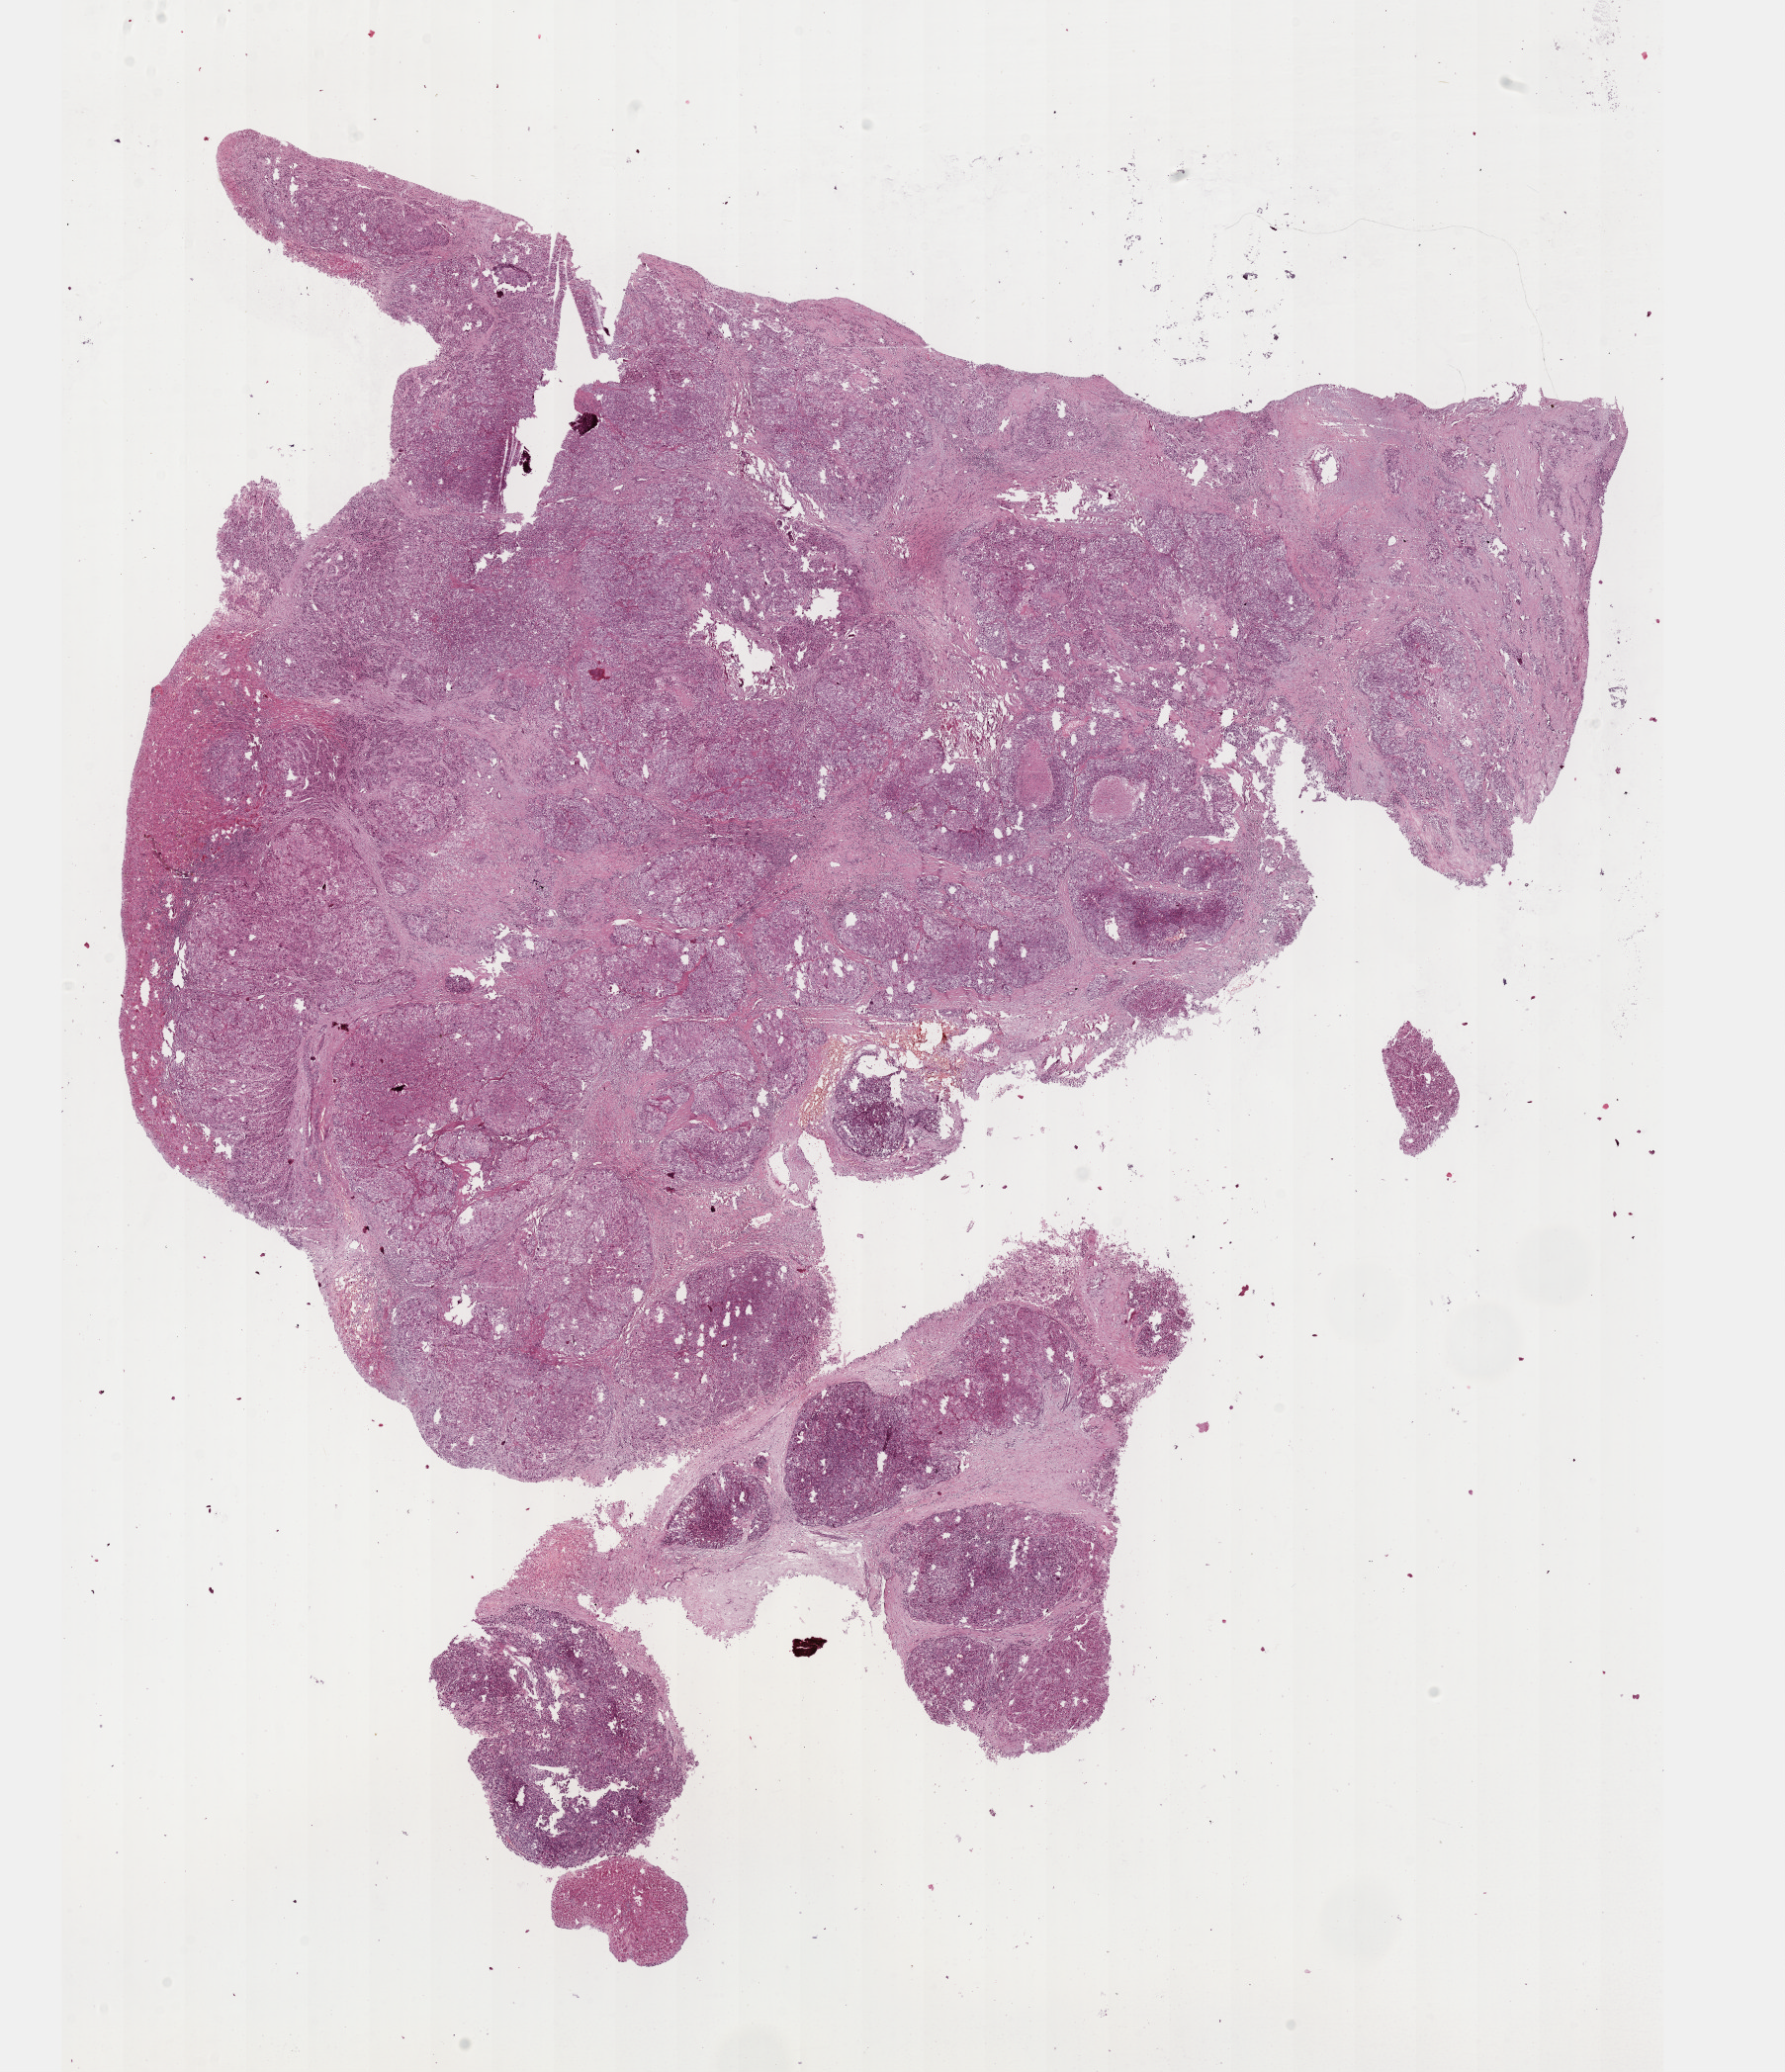
Digitized H&E tissue section (whole slide) — a low-resolution overview of the entire scanned area, about 14.6 x 16.9 mm (from a 40x scan), formalin-fixed paraffin-embedded (FFPE) diagnostic section, sample: primary tumour, liver. Patient: male, age at initial diagnosis 47 years. Histologic grade: G2 (moderately differentiated).
Diagnosis: Hepatocellular carcinoma, NOS. AJCC pathologic stage: II.